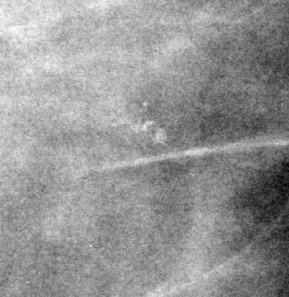
Crop from a digitized film mammogram around one marked abnormality; right breast; CC view.
Calcifications, morphology pleomorphic, distribution clustered; BI-RADS assessment category 4; subtlety rating 3 on a 1 (subtle) to 5 (obvious) scale; pathology result (as recorded, not read from the image): benign.